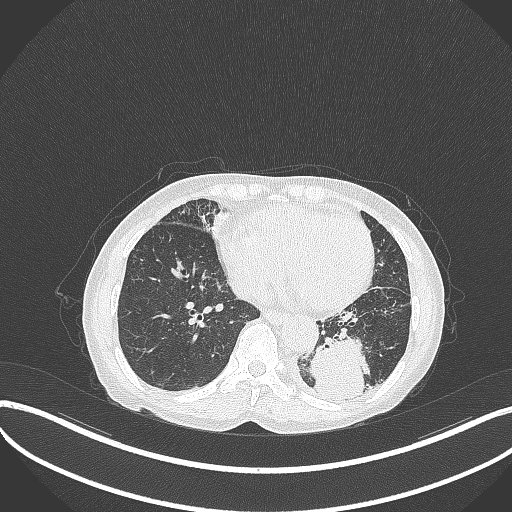
Chest CT, one axial slice. Position 98 of 370 along the scan axis. Reconstruction kernel B70f. Lung window (W 1500 / L -600 HU). 1 mm slice thickness. 512 × 512 image matrix, field of view 400 × 400 mm. Patient: female, 78 years. Case-level facts recorded for this patient, not image findings: clinical TNM (as recorded): T3 N0 M1.
Outlined on this slice (rectangle marked by the reading radiologist):
- lung tumour (recorded histology: squamous cell carcinoma): bounding box (x1, y1, x2, y2) in pixels: (306, 331, 373, 400)